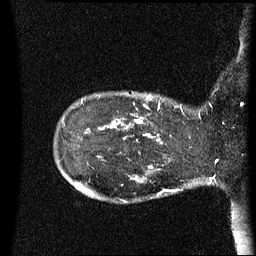
Breast MRI (dynamic contrast-enhanced), one sagittal slice; position 13 of 60 along the scan axis; dynamic contrast-enhanced series, image 2 of 3 at this slice position (ordered by acquisition); 1.5 T; TE 4.2 ms, TR 8.4 ms; 256 × 256 image matrix. Patient: female, 41 years. Case-level facts recorded for this patient, not image findings: setting: breast cancer imaged before/during neoadjuvant chemotherapy; receptor status: HER2-positive.
Outlined on this slice (semi-automatic segmentation, software-assisted and operator-edited):
- analysis volume of interest (the breast-tissue region the enhancement analysis was run in; not a lesion): box from (x=122, y=92) to (x=195, y=137) px
- tumour enhancement mask (voxels above the 70 % enhancement threshold inside the analysis volume of interest): (x=125, y=96)–(x=160, y=137)